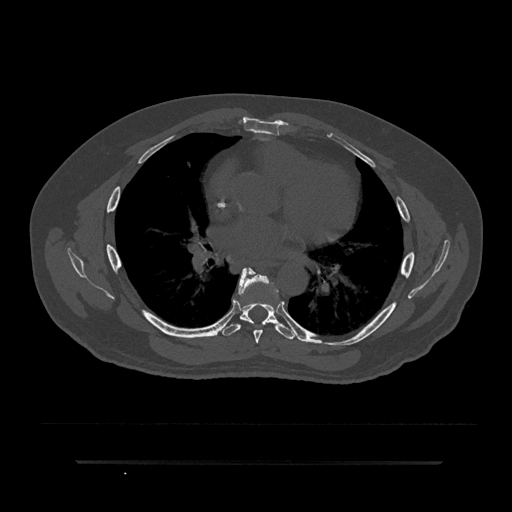
CT including the spine, one axial slice. Position 502 of 797 along the scan axis. Bone window (W 1800 / L 400 HU). 0.5 mm slice thickness. 512 × 512 image matrix. Patient: male, 59 years. From the clinical record (not read from this slice): primary cancer: bile ducts; vertebrae with lytic lesions (as recorded): T10.
Outlined on this slice (semi-automatic segmentation, software-assisted and operator-edited):
- T6 vertebra: bounding box (x1, y1, x2, y2) in pixels: (238, 268, 278, 344)
- T7 vertebra: (222, 268, 295, 339)